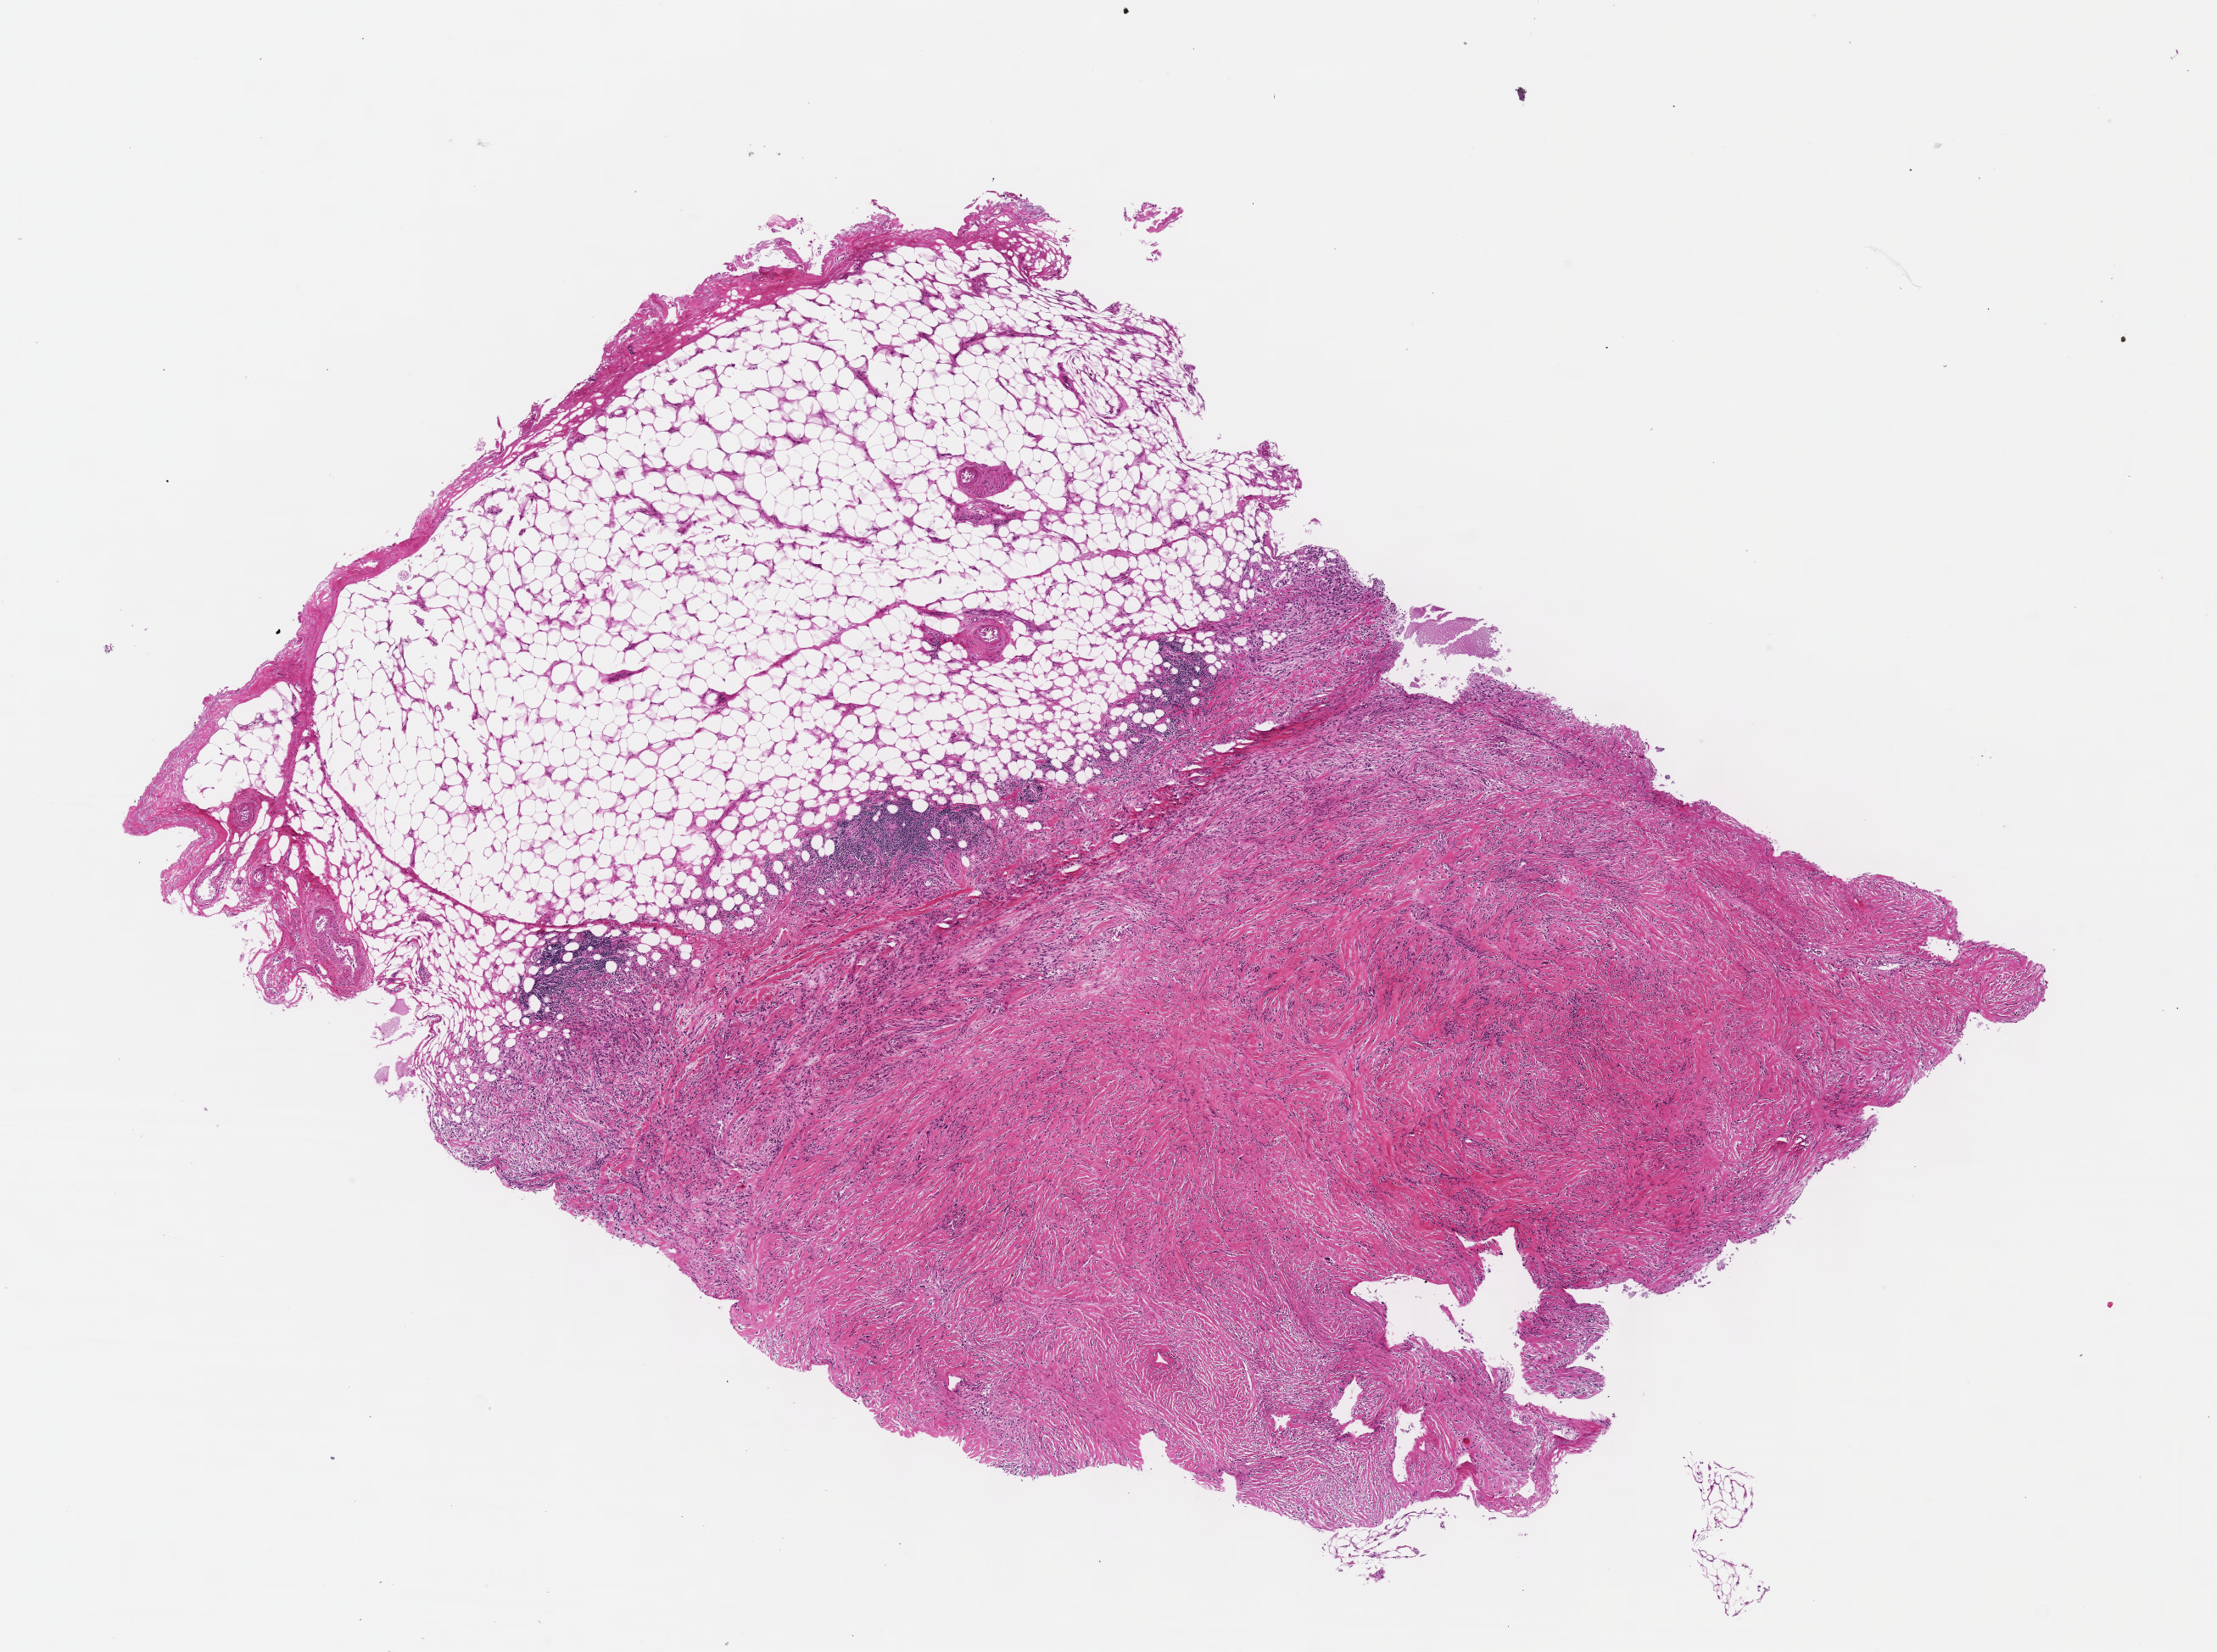
Hematoxylin and eosin (H&E) stained whole-slide image — whole scanned area (about 10.6 x 7.9 mm, acquisition: 40x scan) shown as a low-resolution overview. Formalin-fixed paraffin-embedded (FFPE) diagnostic section. Primary tumour sample from the mesothelium. Male, age 60 years at initial diagnosis.
AJCC pathologic stage: III. Diagnosis: Mesothelioma, biphasic, malignant (pleura, NOS). TNM: T3 NX MX.